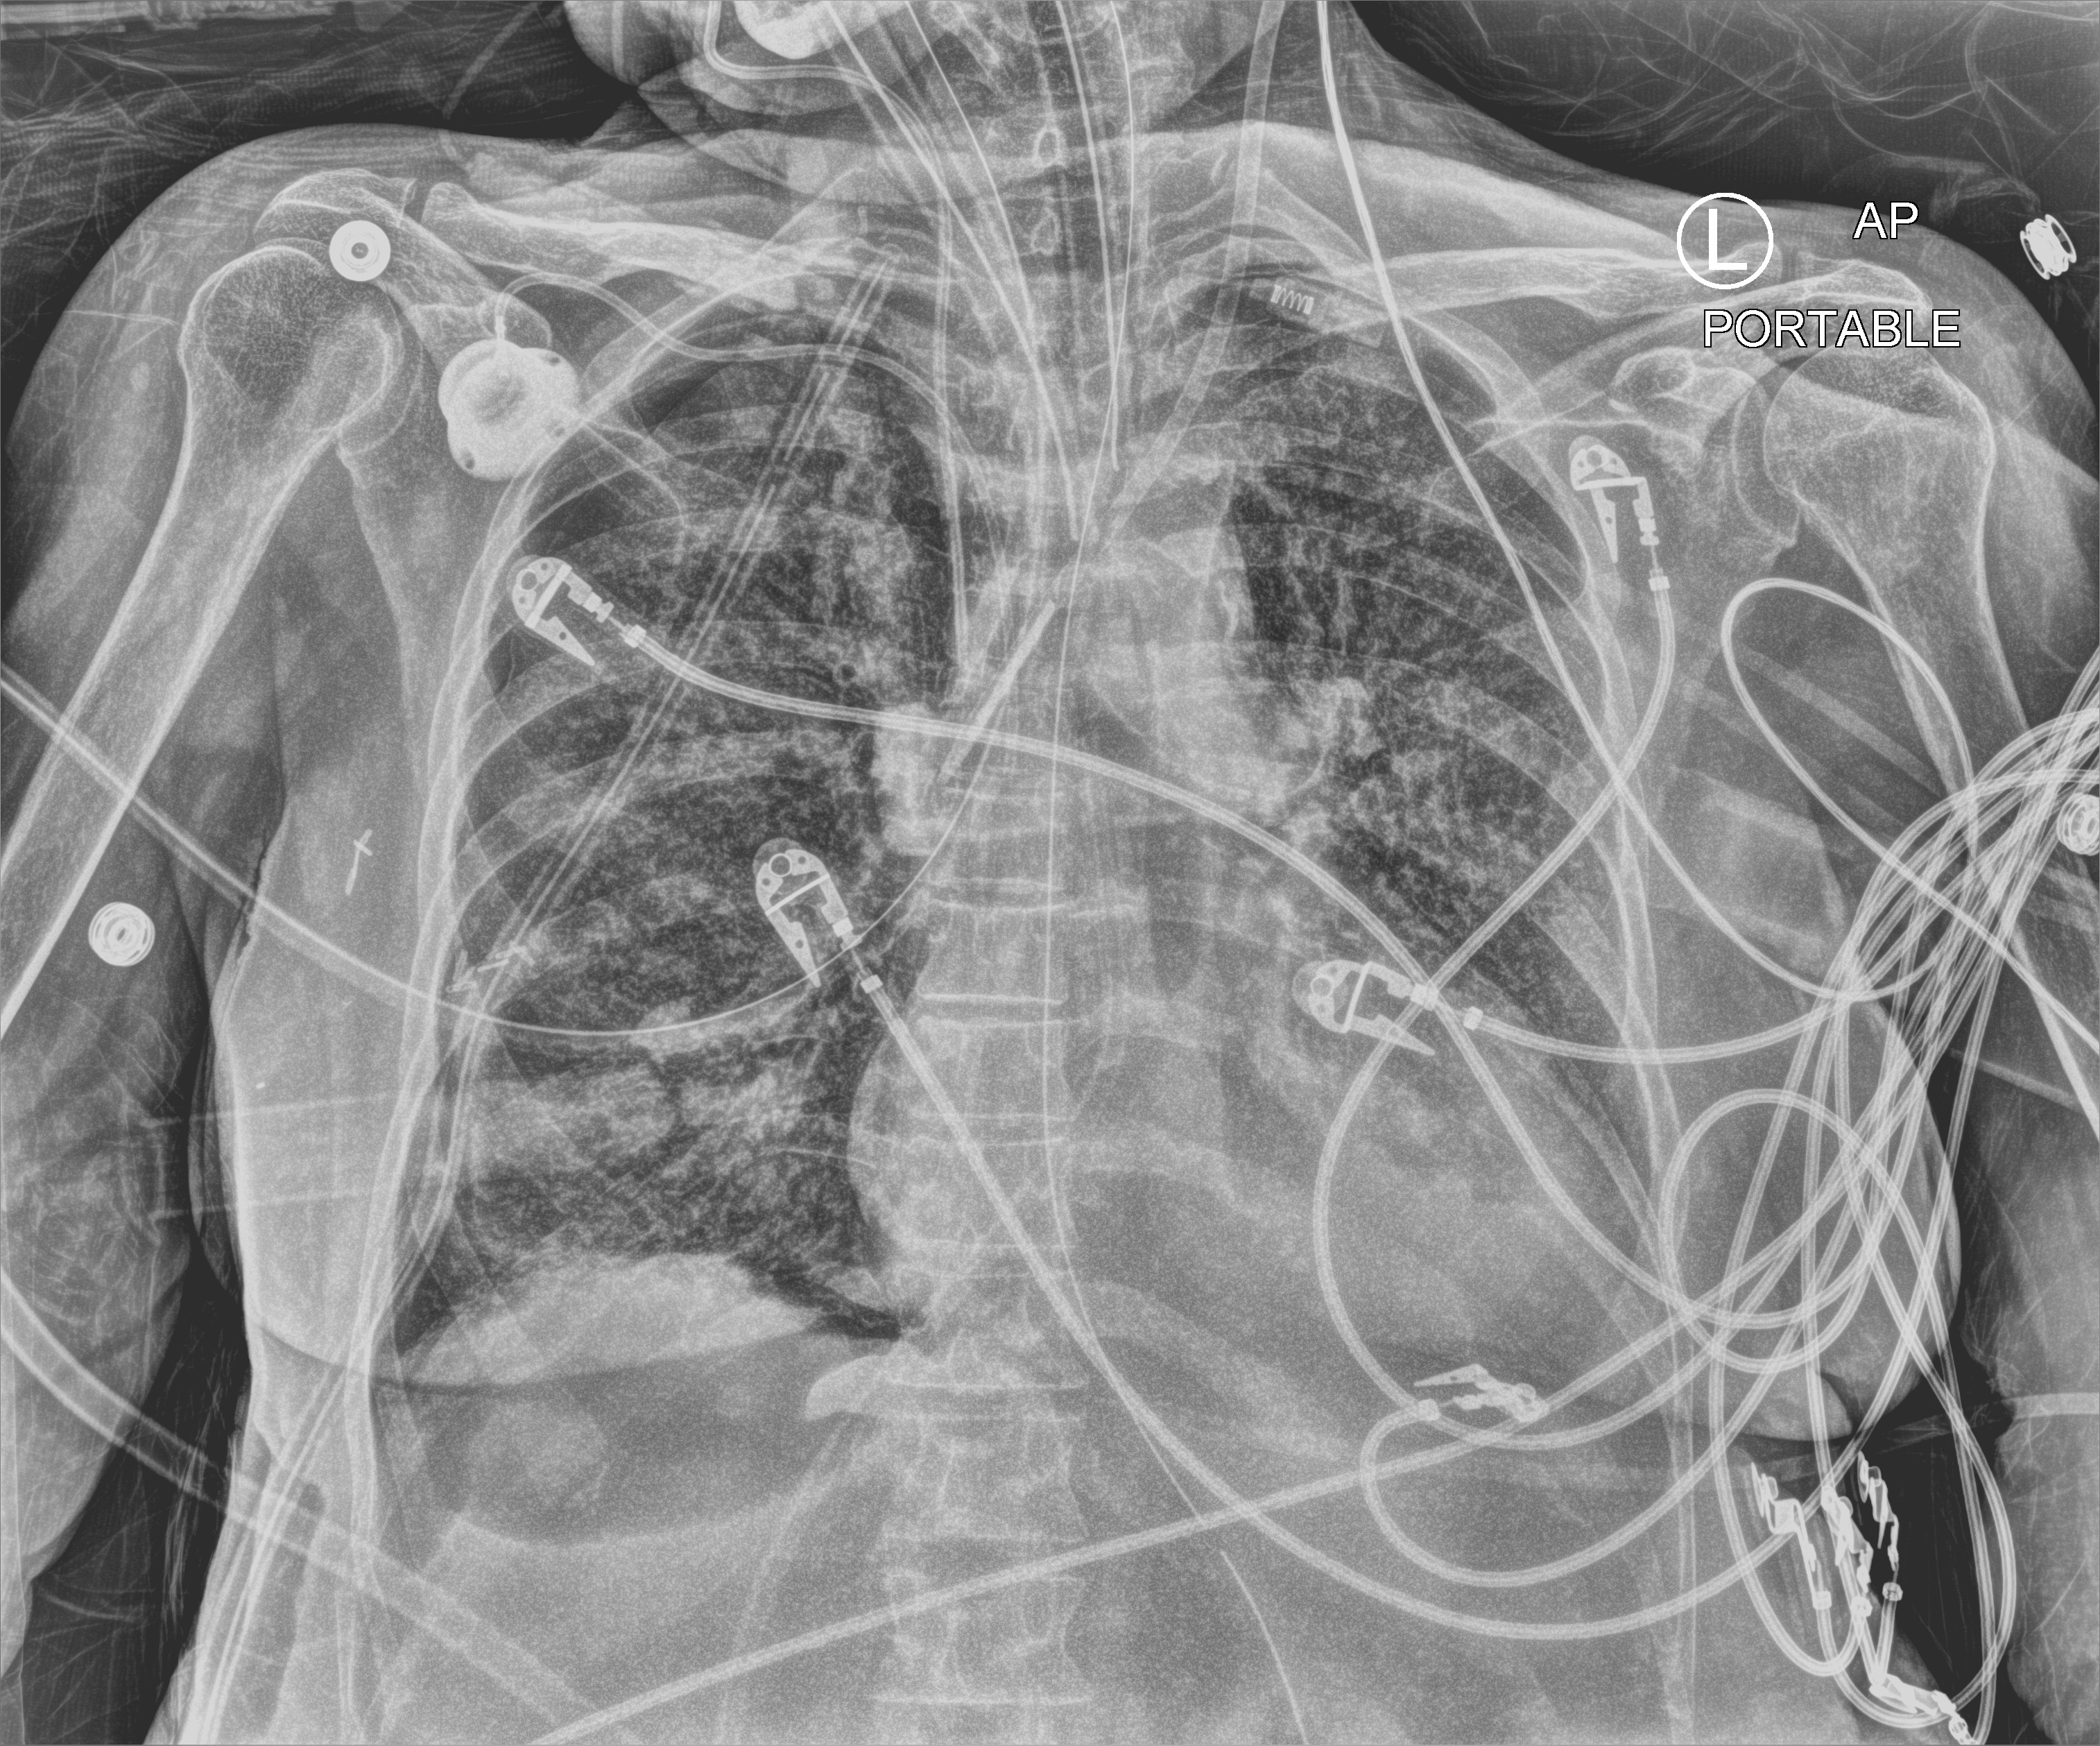
Bedside chest radiograph (computed radiography), anteroposterior (AP) projection. Patient hospitalised with COVID-19; female, aged 60–74 years.
From the hospital-stay record, not from the radiograph (when in the stay this image was taken is not recorded): chronic kidney disease (admission record): no.